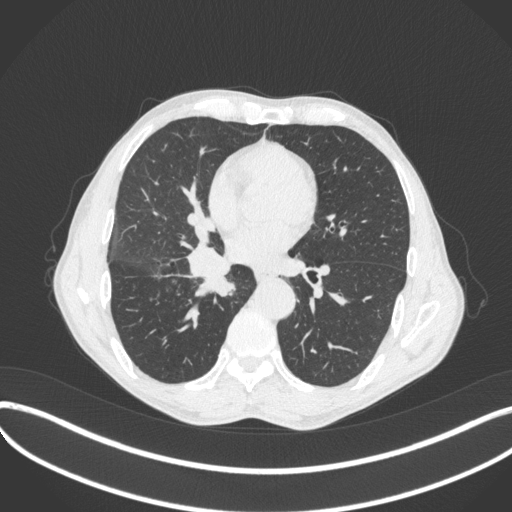
Chest CT, one axial slice. Position 203 of 481 along the scan axis. Reconstruction kernel B31f. 120 kVp. Lung window (W 1500 / L -600 HU). 512 × 512 image matrix, field of view 400 × 400 mm. Male patient, age 65 years. Case-level facts recorded for this patient, not image findings: clinical TNM (as recorded): T2a N0 M0.
Structures marked on this image (rectangle marked by the reading radiologist):
- lung tumour (recorded histology: squamous cell carcinoma): box from (x=186, y=246) to (x=244, y=303) px